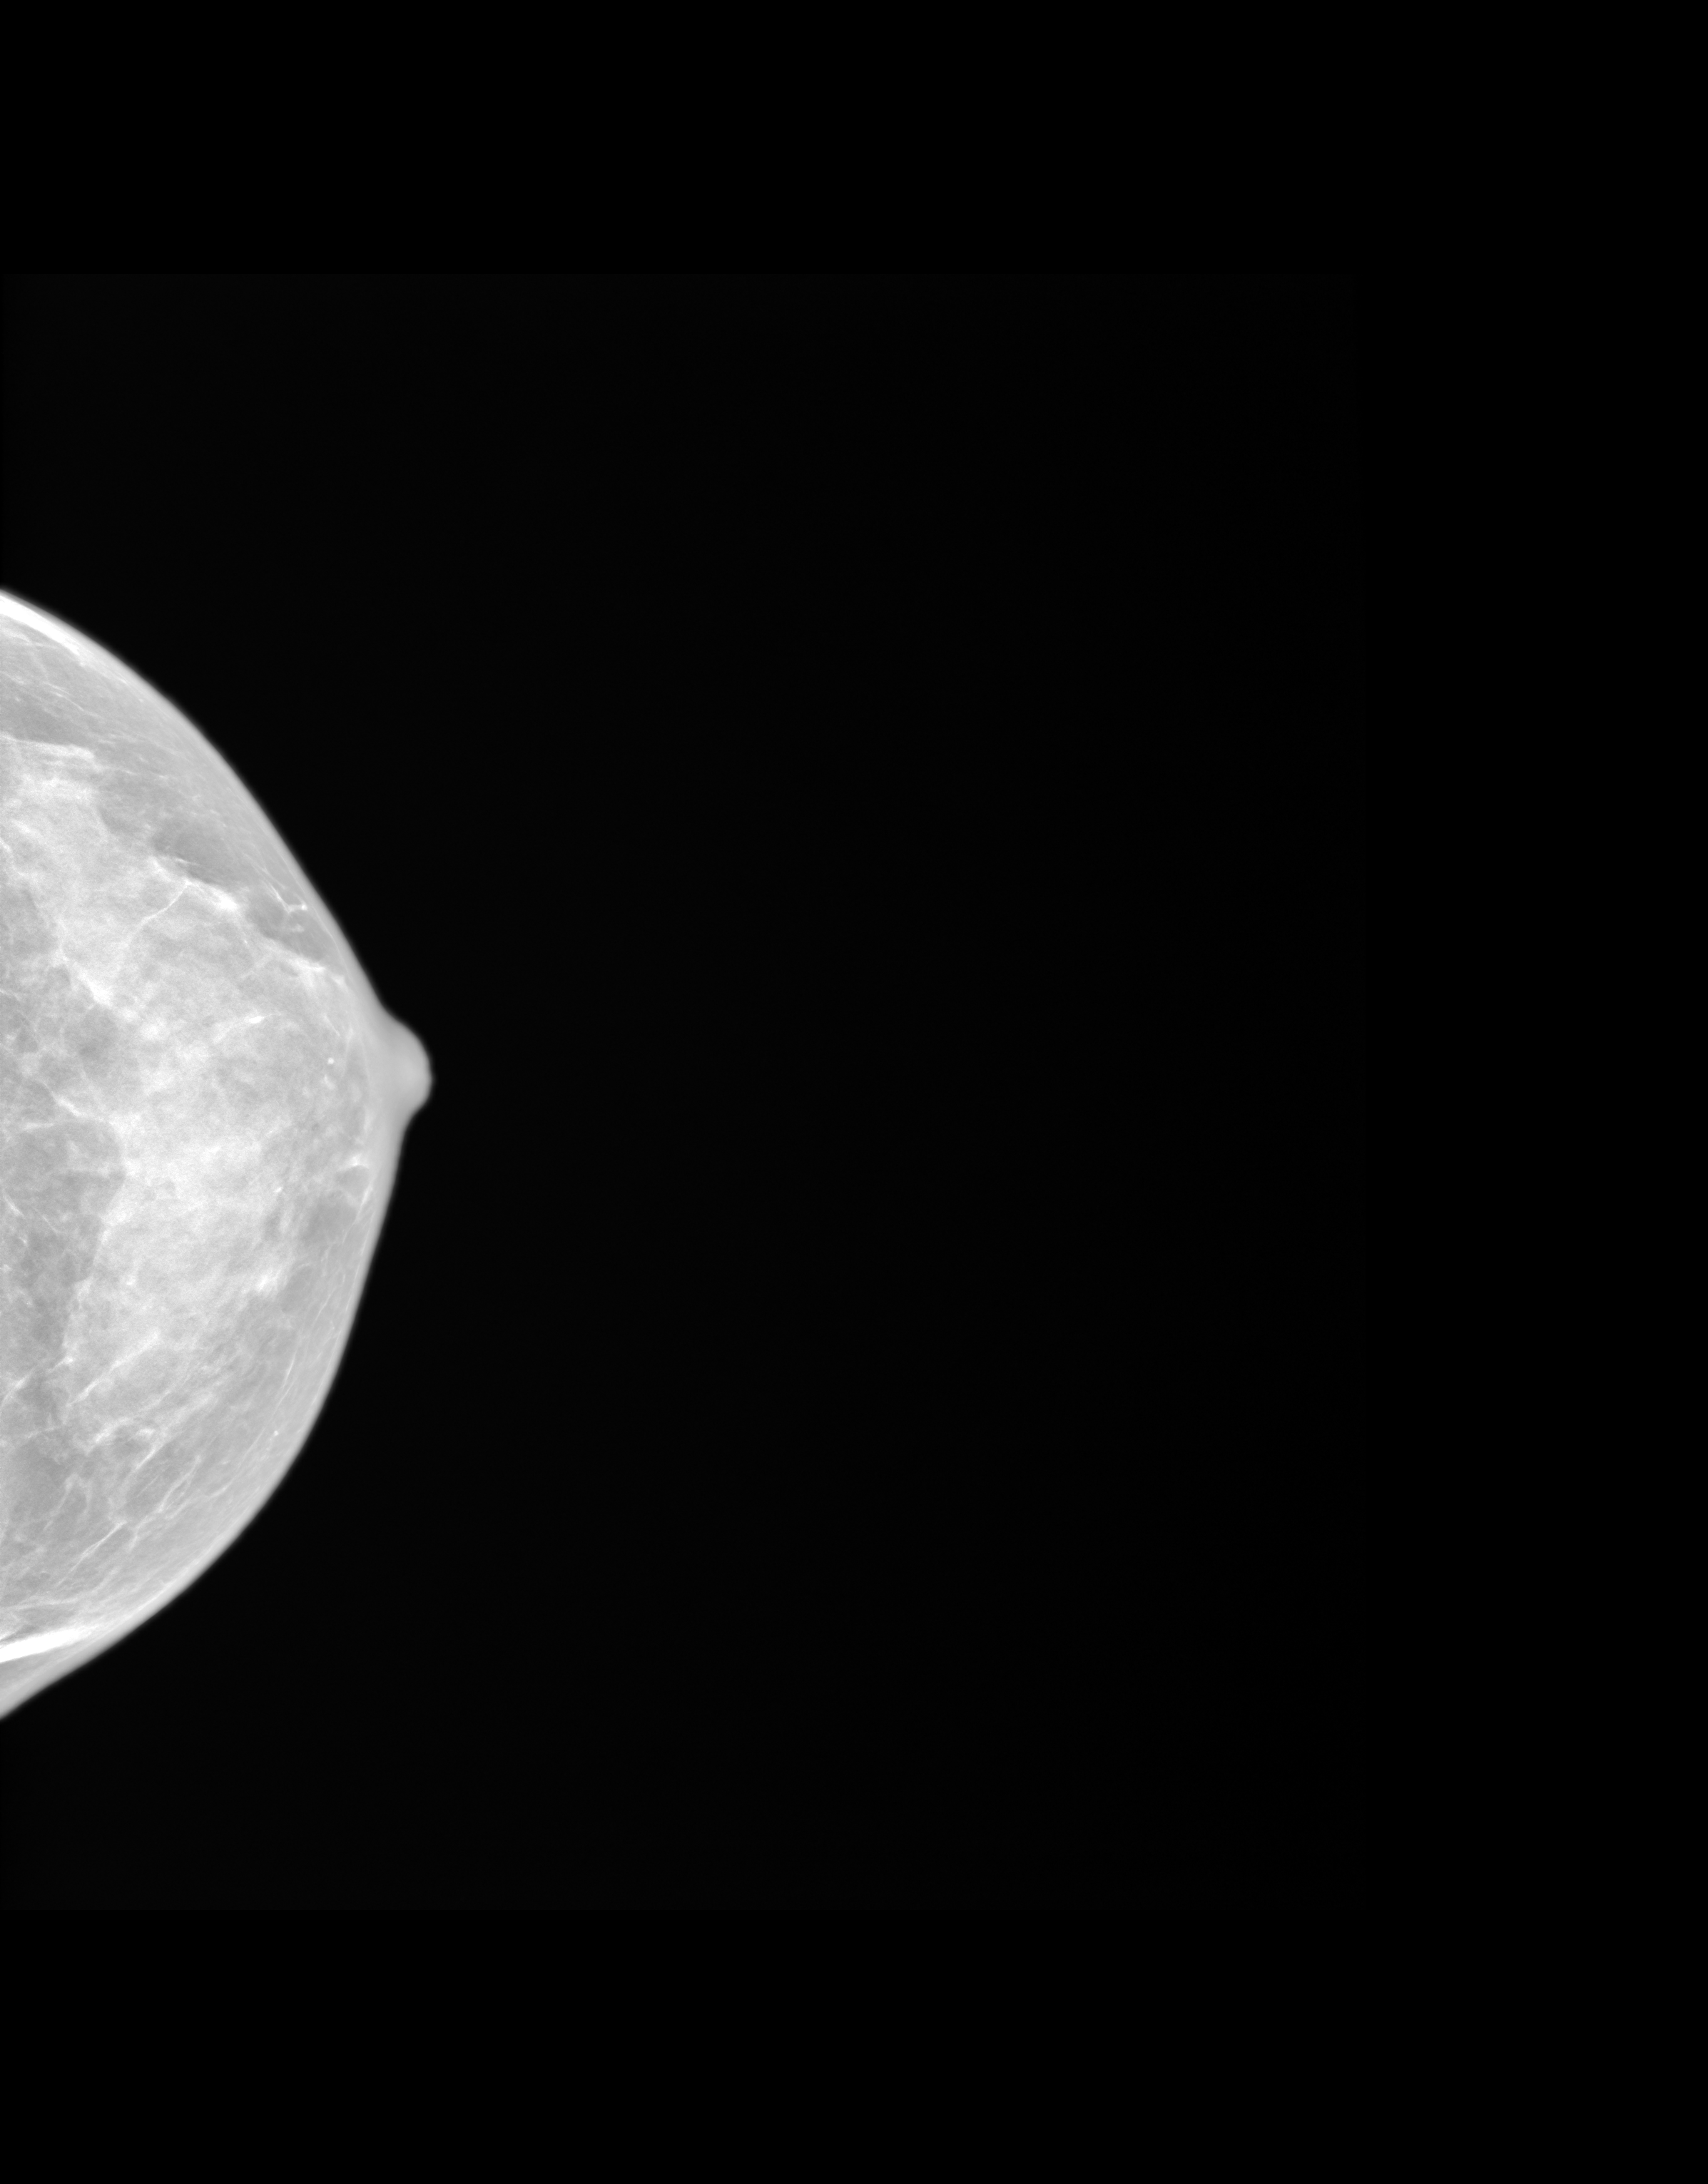
Synthesized 2-D mammogram reconstructed from digital breast tomosynthesis, left breast, CC view, annual screening mammography examination, system: SenoIris_1SP1.1(421). Female patient, age 55 years.
BI-RADS breast density category at the screening exam (both breasts, scale 1–4): 4. Final BI-RADS assessment for this screening round (tomosynthesis exam, both breasts): category 1. Recall: no recall after this screen.